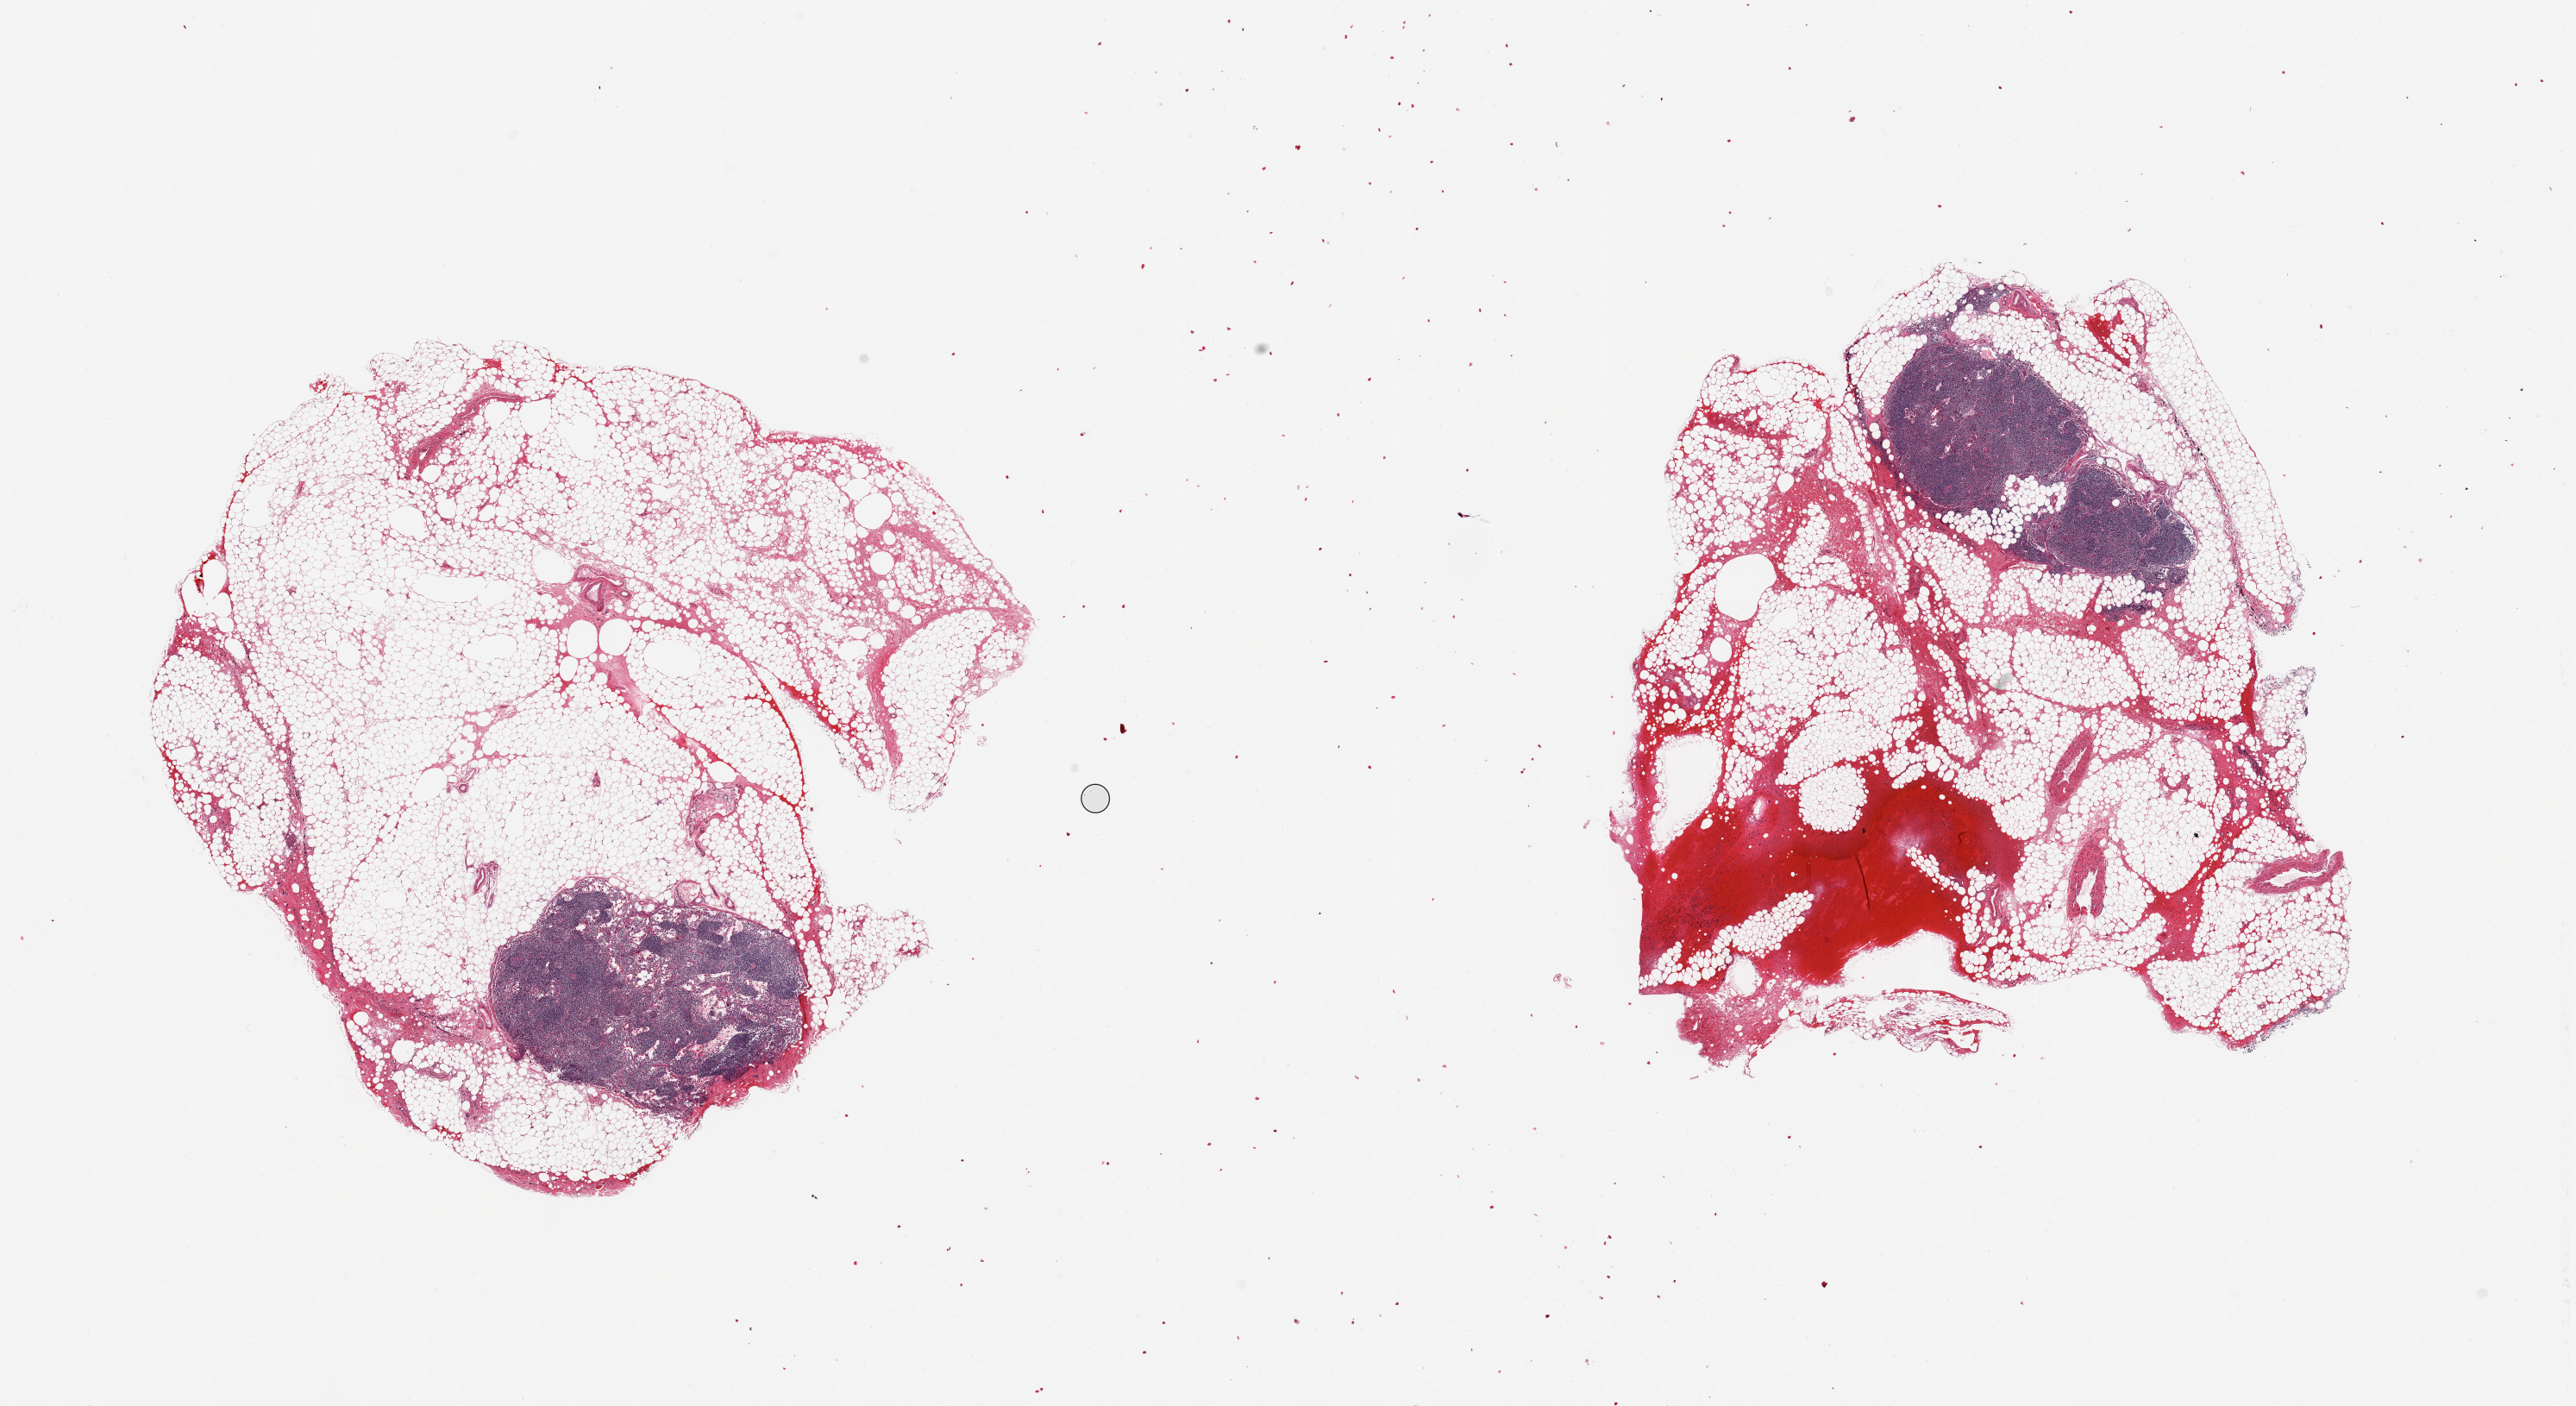
Digitized hematoxylin and eosin (H&E)-stained section, brightfield — a low-resolution overview of the entire scanned area, about 23.6 x 12.9 mm (acquisition: 20x scan); PAXgene-fixed, paraffin-embedded tissue; sampled site (target tissue): thyroid; tissue donor sample. Donor: female.
Review note (as recorded): 2 pieces; lymph nodes & fat, no thyroid.